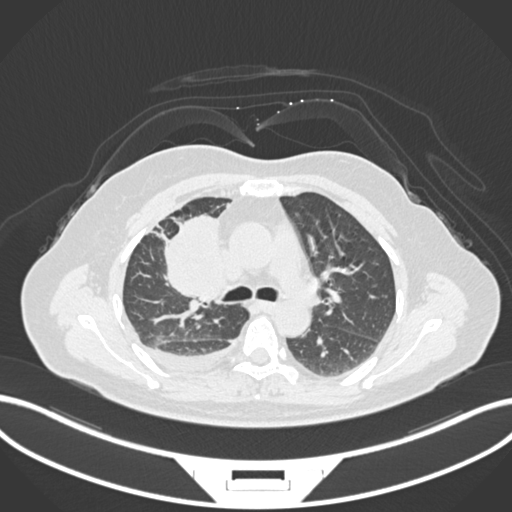
Chest CT, one axial slice. Position 96 of 172 along the scan axis. 120 kVp. Lung window (W 1500 / L -600 HU). 1 mm slice thickness. 512 × 512 image matrix. Female patient, age 52 years. Case-level facts recorded for this patient, not image findings: clinical TNM (as recorded): T3 N1 M1.
Outlined on this slice (rectangle marked by the reading radiologist):
- lung tumour (recorded histology: adenocarcinoma): bounding box (x1, y1, x2, y2) in pixels: (155, 212, 222, 307)